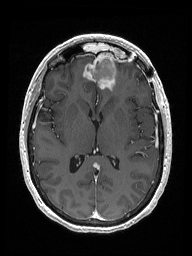
Brain MRI from a brain-tumour surgery series, one axial slice; slice 83 of 192 in the series (ordered by position); T1-weighted post-contrast; 1 mm slice thickness; 192 × 256 image matrix, field of view 187 × 250 mm. Case-level facts recorded for this patient, not image findings: histopathology: Metastastic Carcinoma from Breast primary.
Annotated regions visible in this slice (manually delineated by an expert):
- previous resection cavity: bounding box [x1, y1, x2, y2] px = [85, 52, 116, 81]